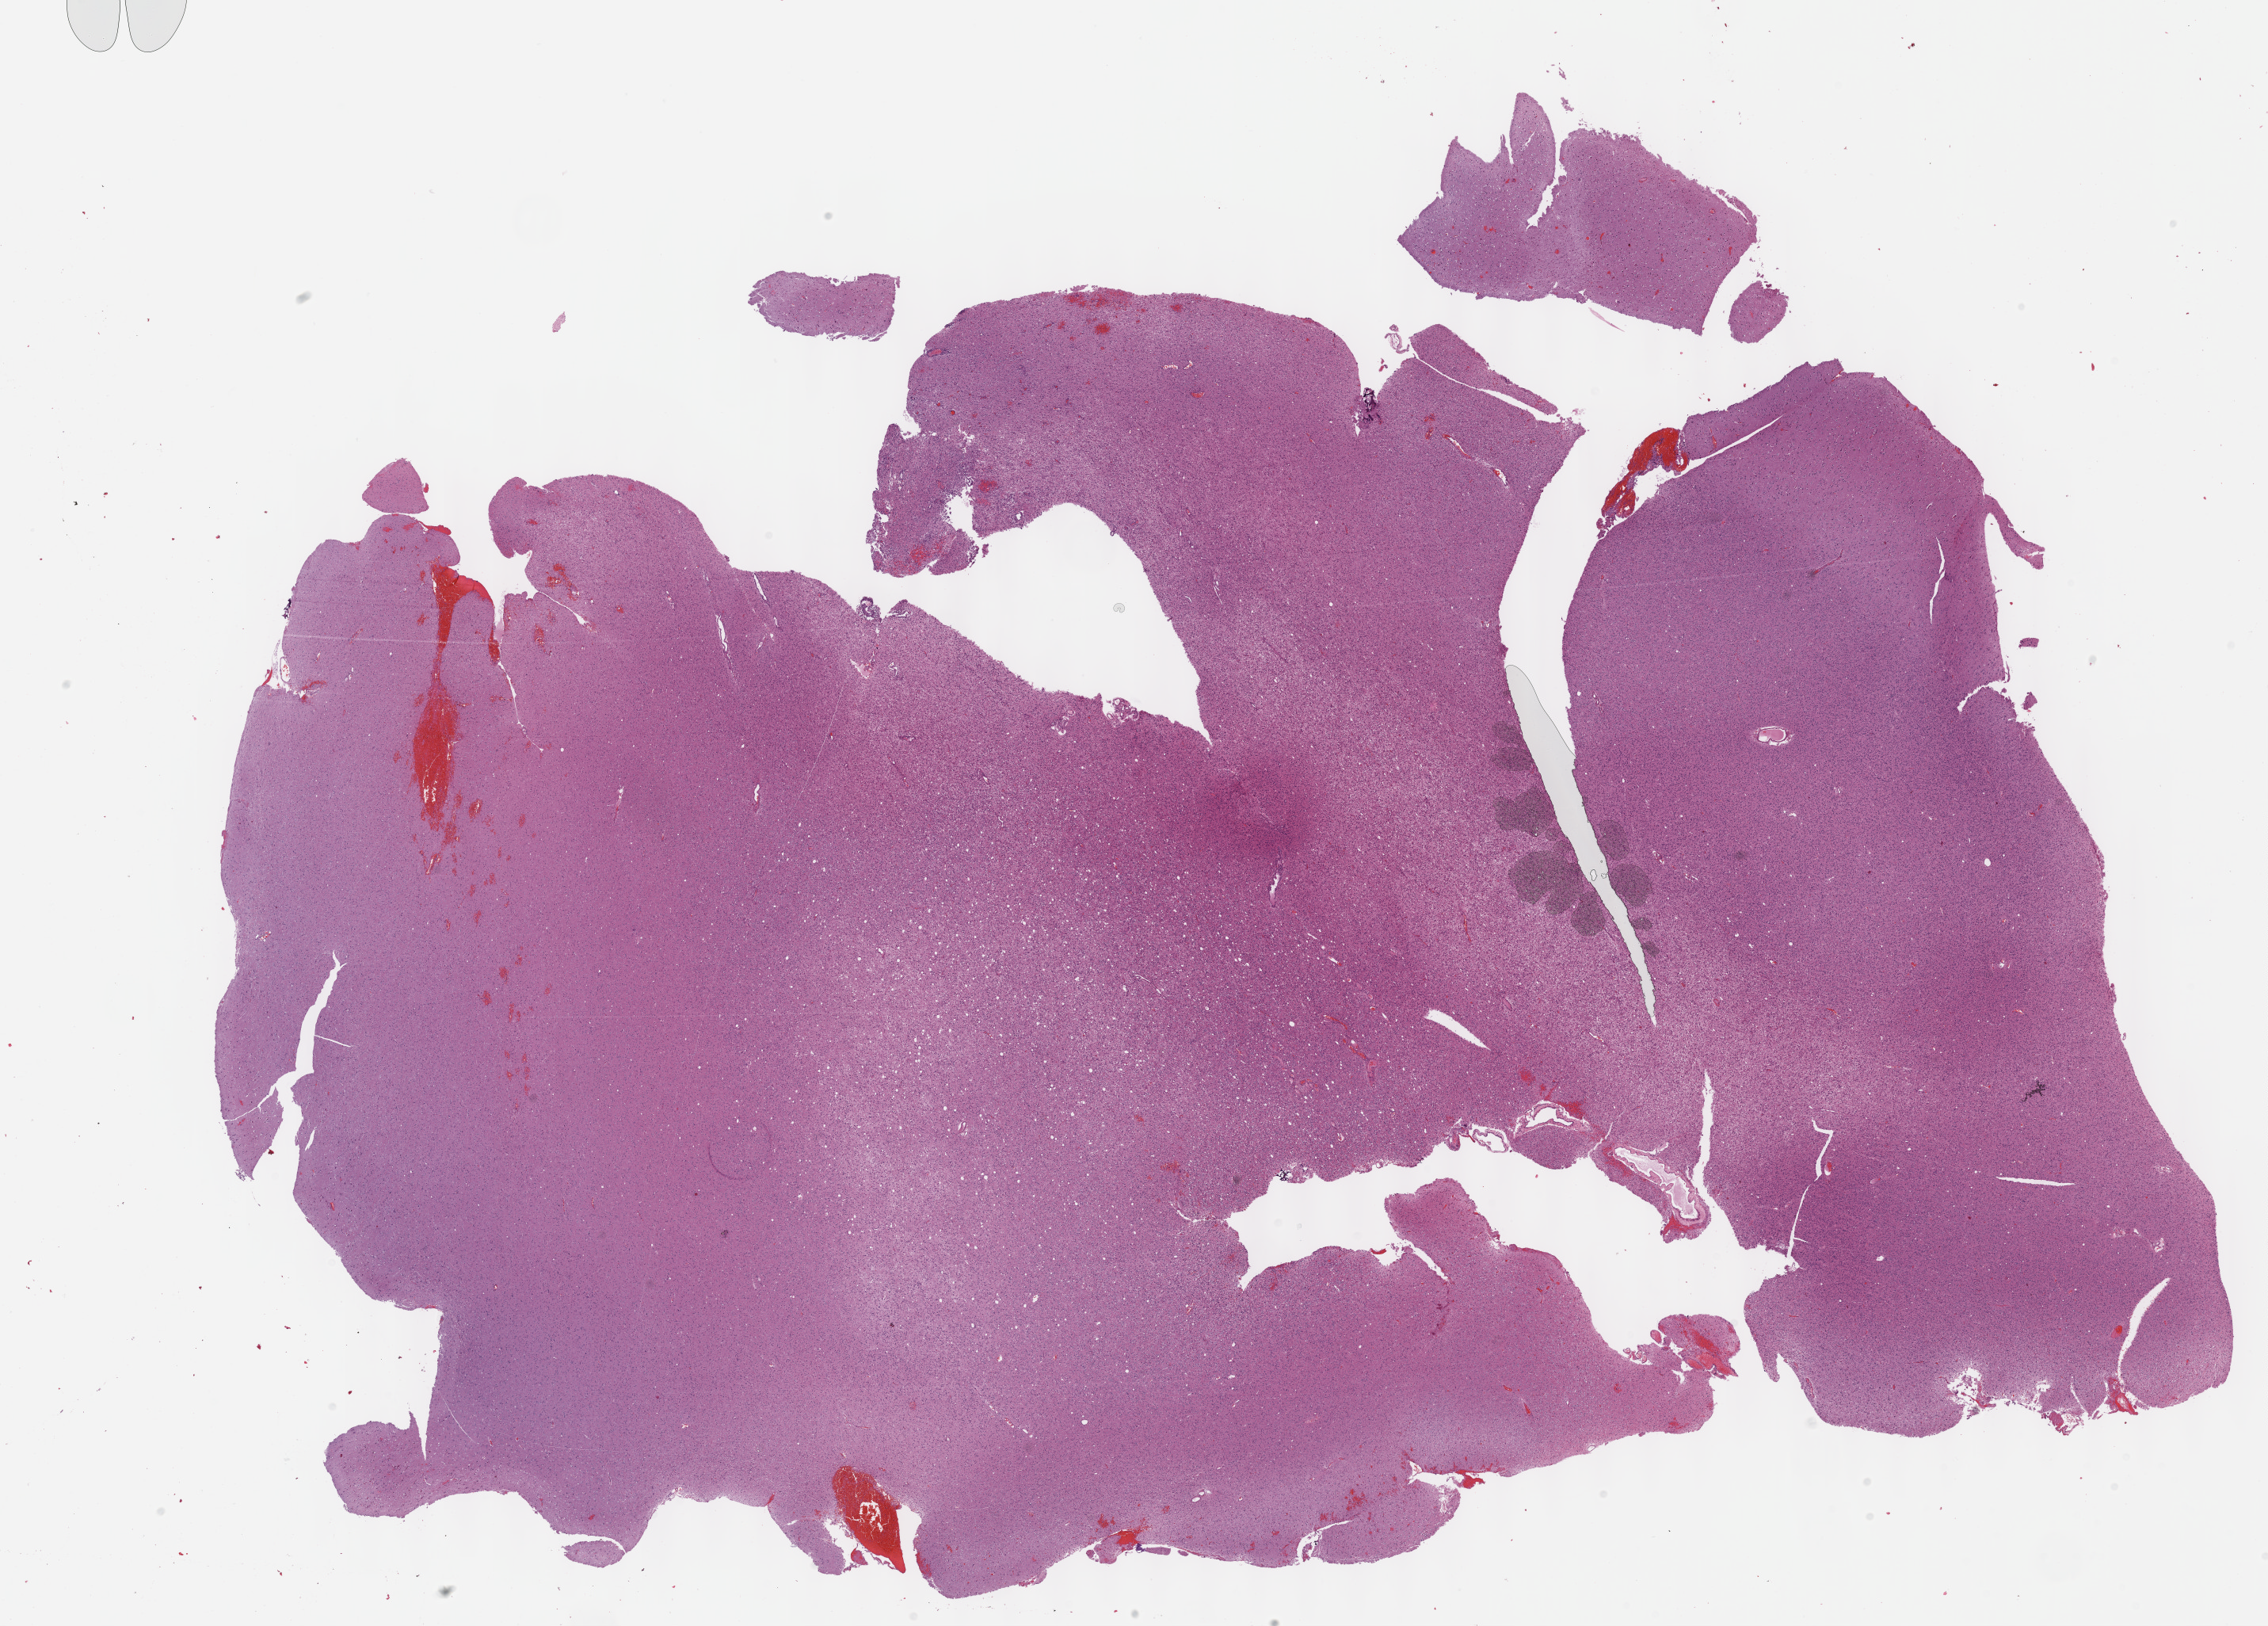
Digitized Hematoxylin and eosin (H&E) stained tissue section (whole slide) — low-resolution overview of the scanned area, about 23.1 x 16.6 mm, formalin-fixed paraffin-embedded (FFPE) diagnostic section, sample: primary tumour, brain. Patient: female, age at initial diagnosis 34 years. Histologic grade: G3 (poorly differentiated).
• pathologic diagnosis: Oligodendroglioma, anaplastic (cerebrum)
• laterality: right